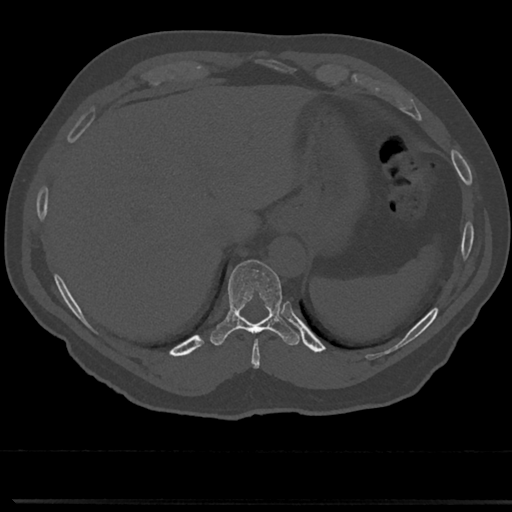
CT including the spine, one axial slice. Slice 262 of 817 in the series (ordered by position). Bone window (W 1800 / L 400 HU). 0.5 mm slice thickness. 512 × 512 image matrix. Patient: male, 61 years. Case-level facts recorded for this patient, not image findings: primary cancer: prostate.
Outlined on this slice (semi-automatically segmented with operator editing):
- T10 vertebra: box from (x=214, y=261) to (x=296, y=343) px
- T9 vertebra: (x=248, y=331)–(x=265, y=356)